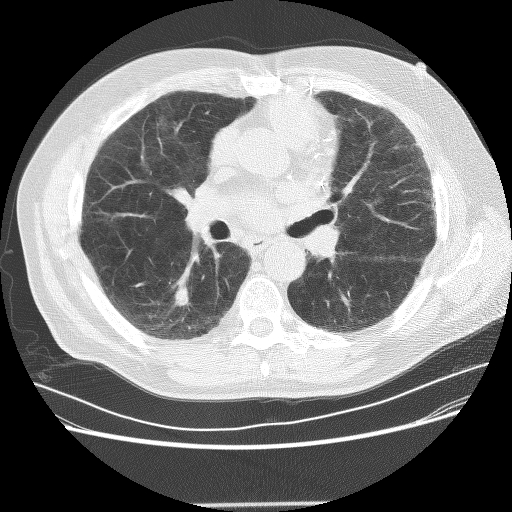
Axial slice from a low-dose chest CT screening exam, first (baseline) screen, lung window (W 1500 / L -600 HU), lung (sharp) reconstruction kernel (BONE), 120 kVp, slice 124 of 281 in the series, 512 × 512 image matrix. Male, age 72 years at enrolment.
Lesion marked by an expert reader, bounding box <154,277,201,322> (left, top, right, bottom; pixels). The screening reader recorded 2 non-calcified nodules or masses ≥4 mm on this exam (right lower lobe, left lower lobe); which of them this box marks is not recorded. Participant outcome: lung cancer diagnosed 436 days after this screen (after the second annual screen) — squamous cell carcinoma, NOS, right lower lobe, poorly differentiated (G3), stage IB (AJCC 6th edition), 42 mm at pathology.